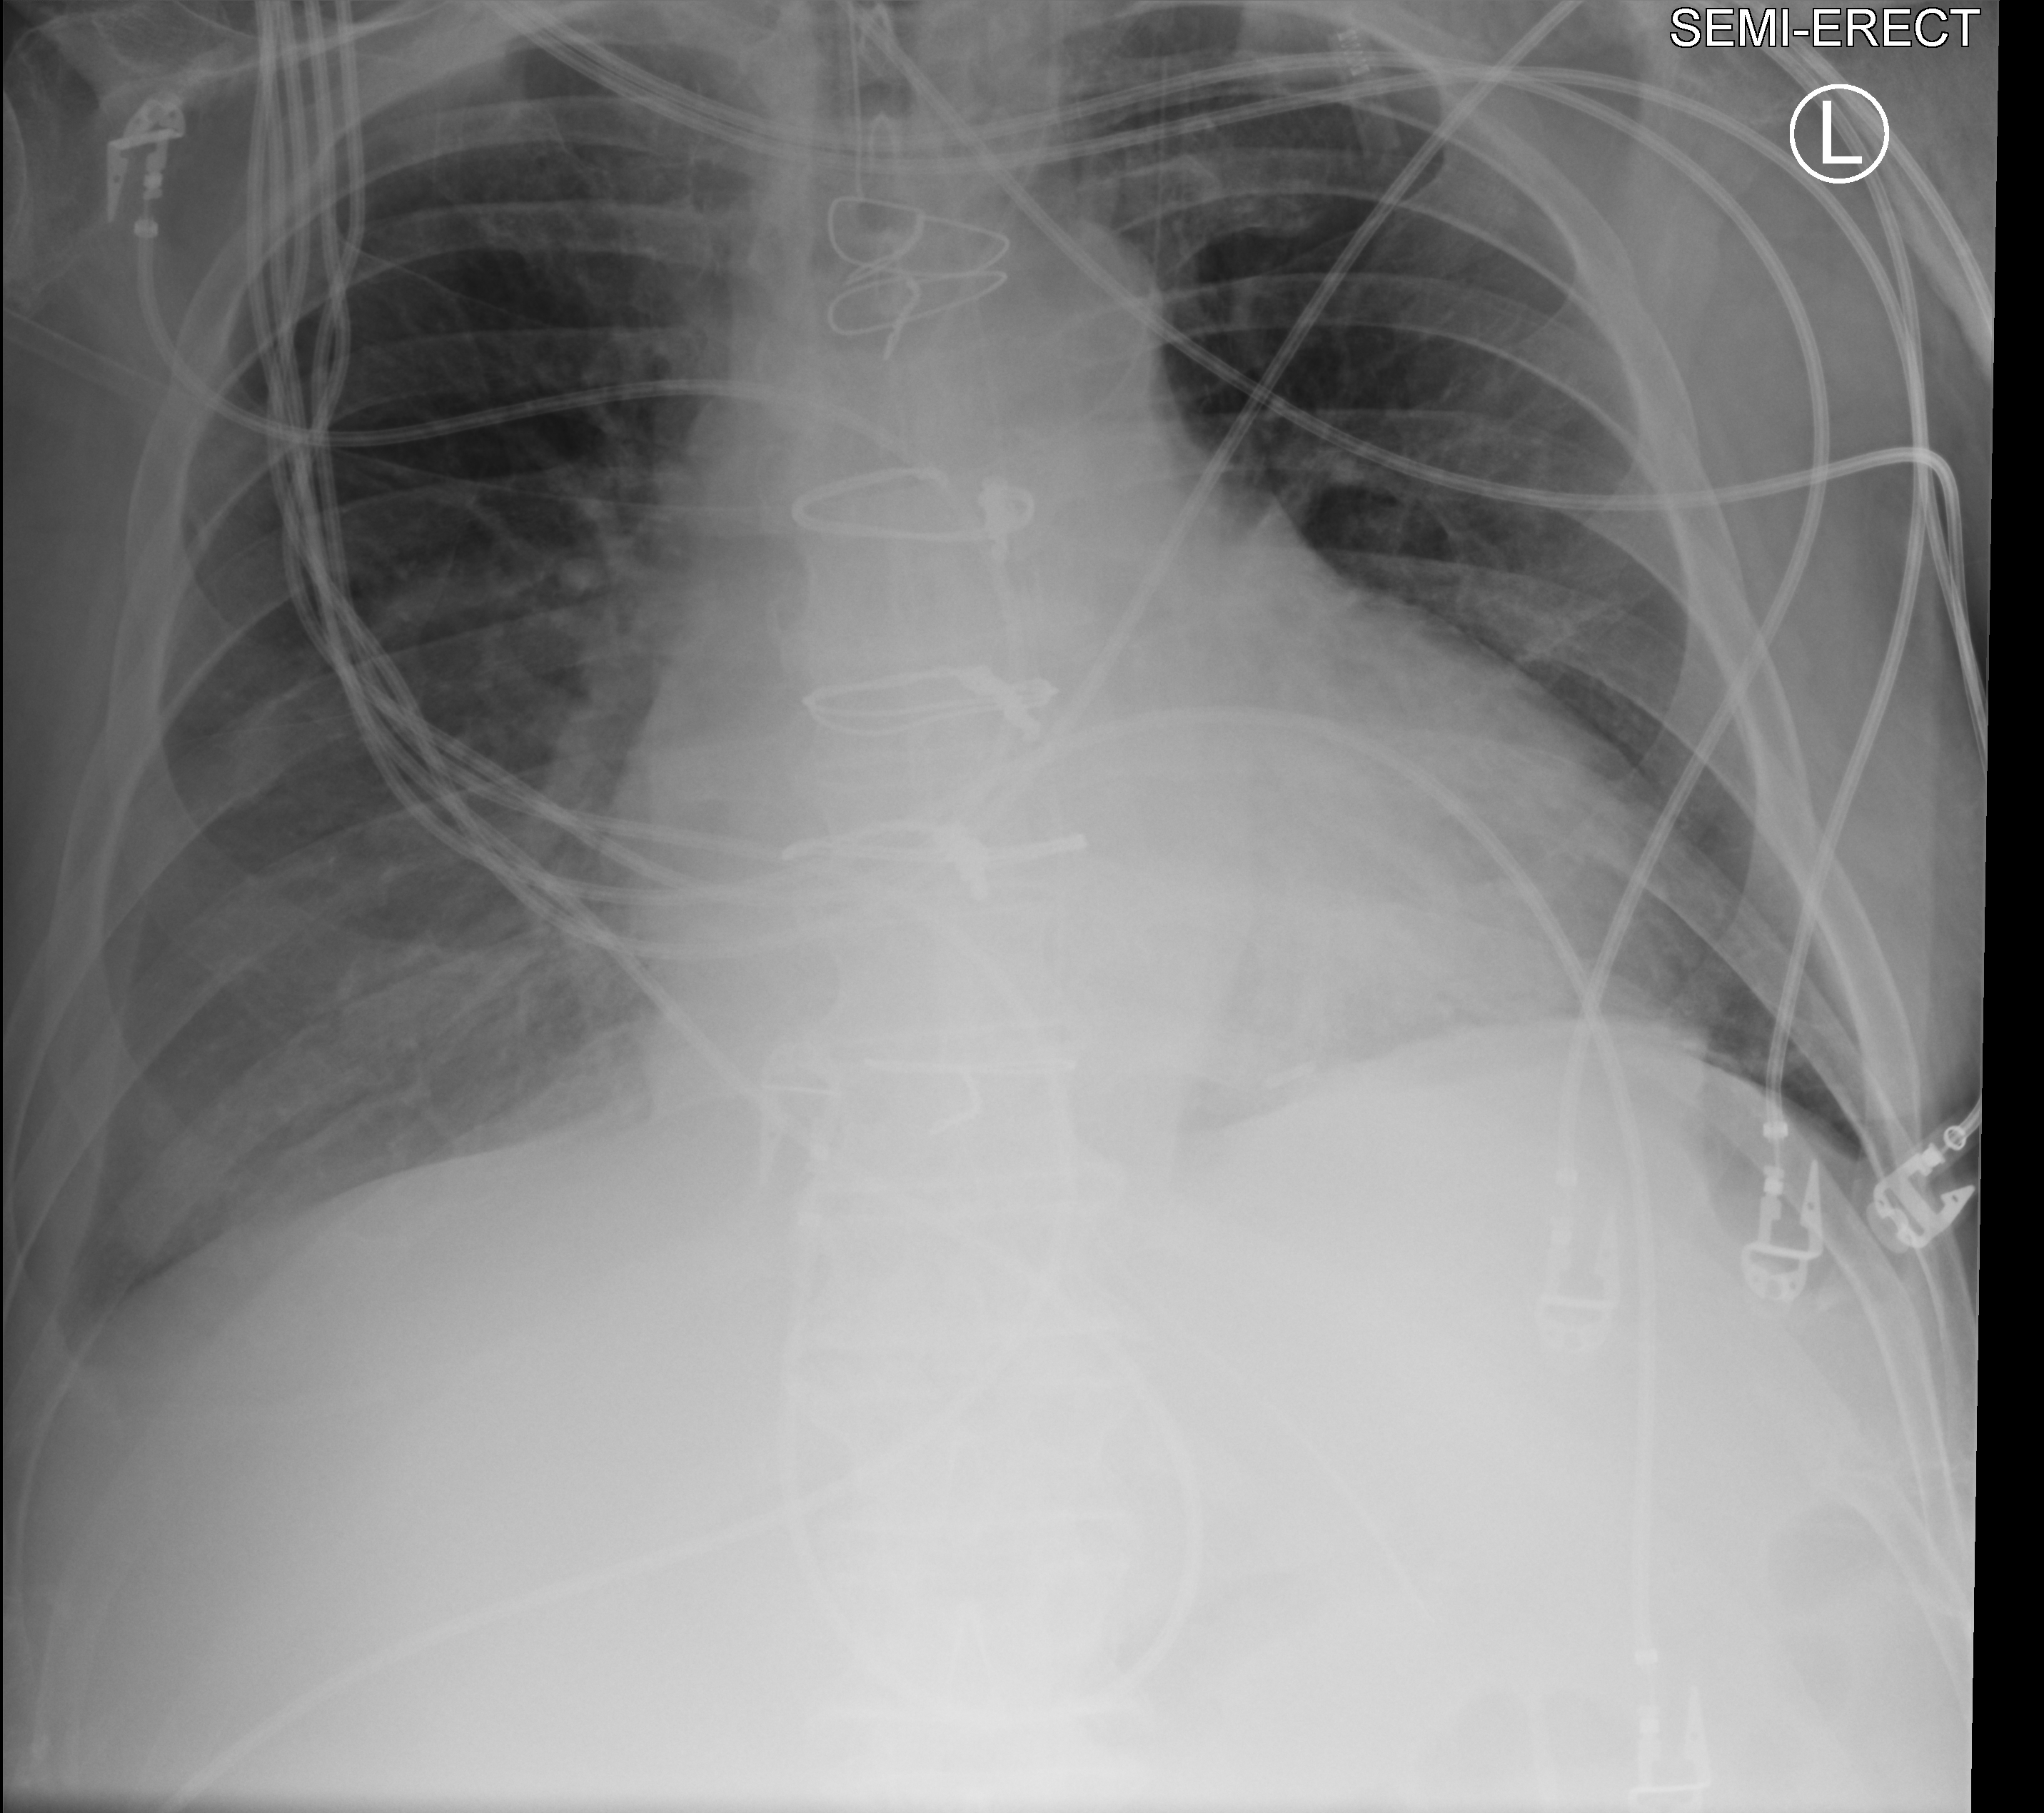
Bedside chest radiograph (computed radiography). Patient hospitalised with COVID-19; male, aged 60–74 years.
Admission-level facts for this patient (not findings on this image; timing relative to this image not recorded):
- admitted to intensive care during this hospital stay: yes
- length of hospital stay: 16 days